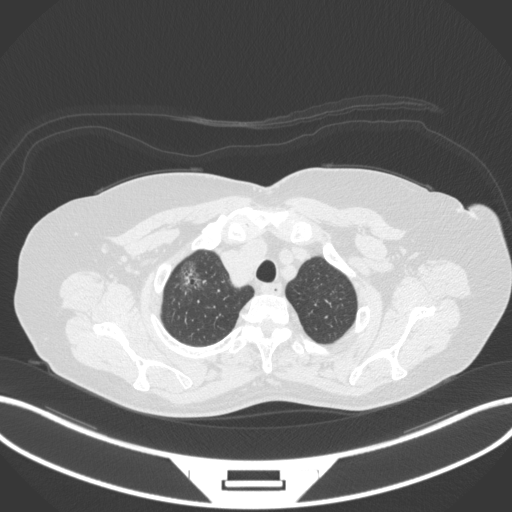
Chest CT, one axial slice. Reconstruction kernel B31f. 120 kVp. Lung window (W 1500 / L -600 HU). 512 × 512 image matrix, field of view 400 × 400 mm. Patient: female, 62 years. Case-level facts recorded for this patient, not image findings: clinical TNM (as recorded): T1c N0 M0.
Structures marked on this image (bounding box drawn by a radiologist):
- lung tumour (recorded histology: adenocarcinoma): box from (x=173, y=256) to (x=212, y=301) px